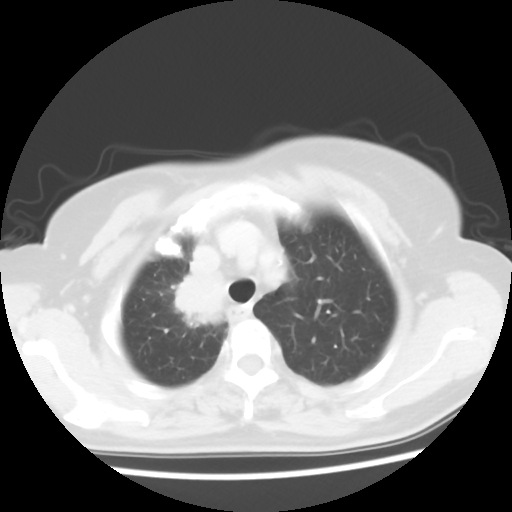
Chest CT, one axial slice; position 46 of 56 along the scan axis; reconstruction kernel STANDARD; 120 kVp; lung window (W 1500 / L -600 HU); 5 mm slice thickness; 512 × 512 image matrix, field of view 314 × 314 mm. Patient: female, 62 years. From the clinical record (not read from this slice): clinical TNM (as recorded): T2 N1 M1a.
Annotated regions visible in this slice (rectangle marked by the reading radiologist):
- lung tumour (recorded histology: adenocarcinoma): bounding box <165,268,228,331> (left, top, right, bottom; pixels)